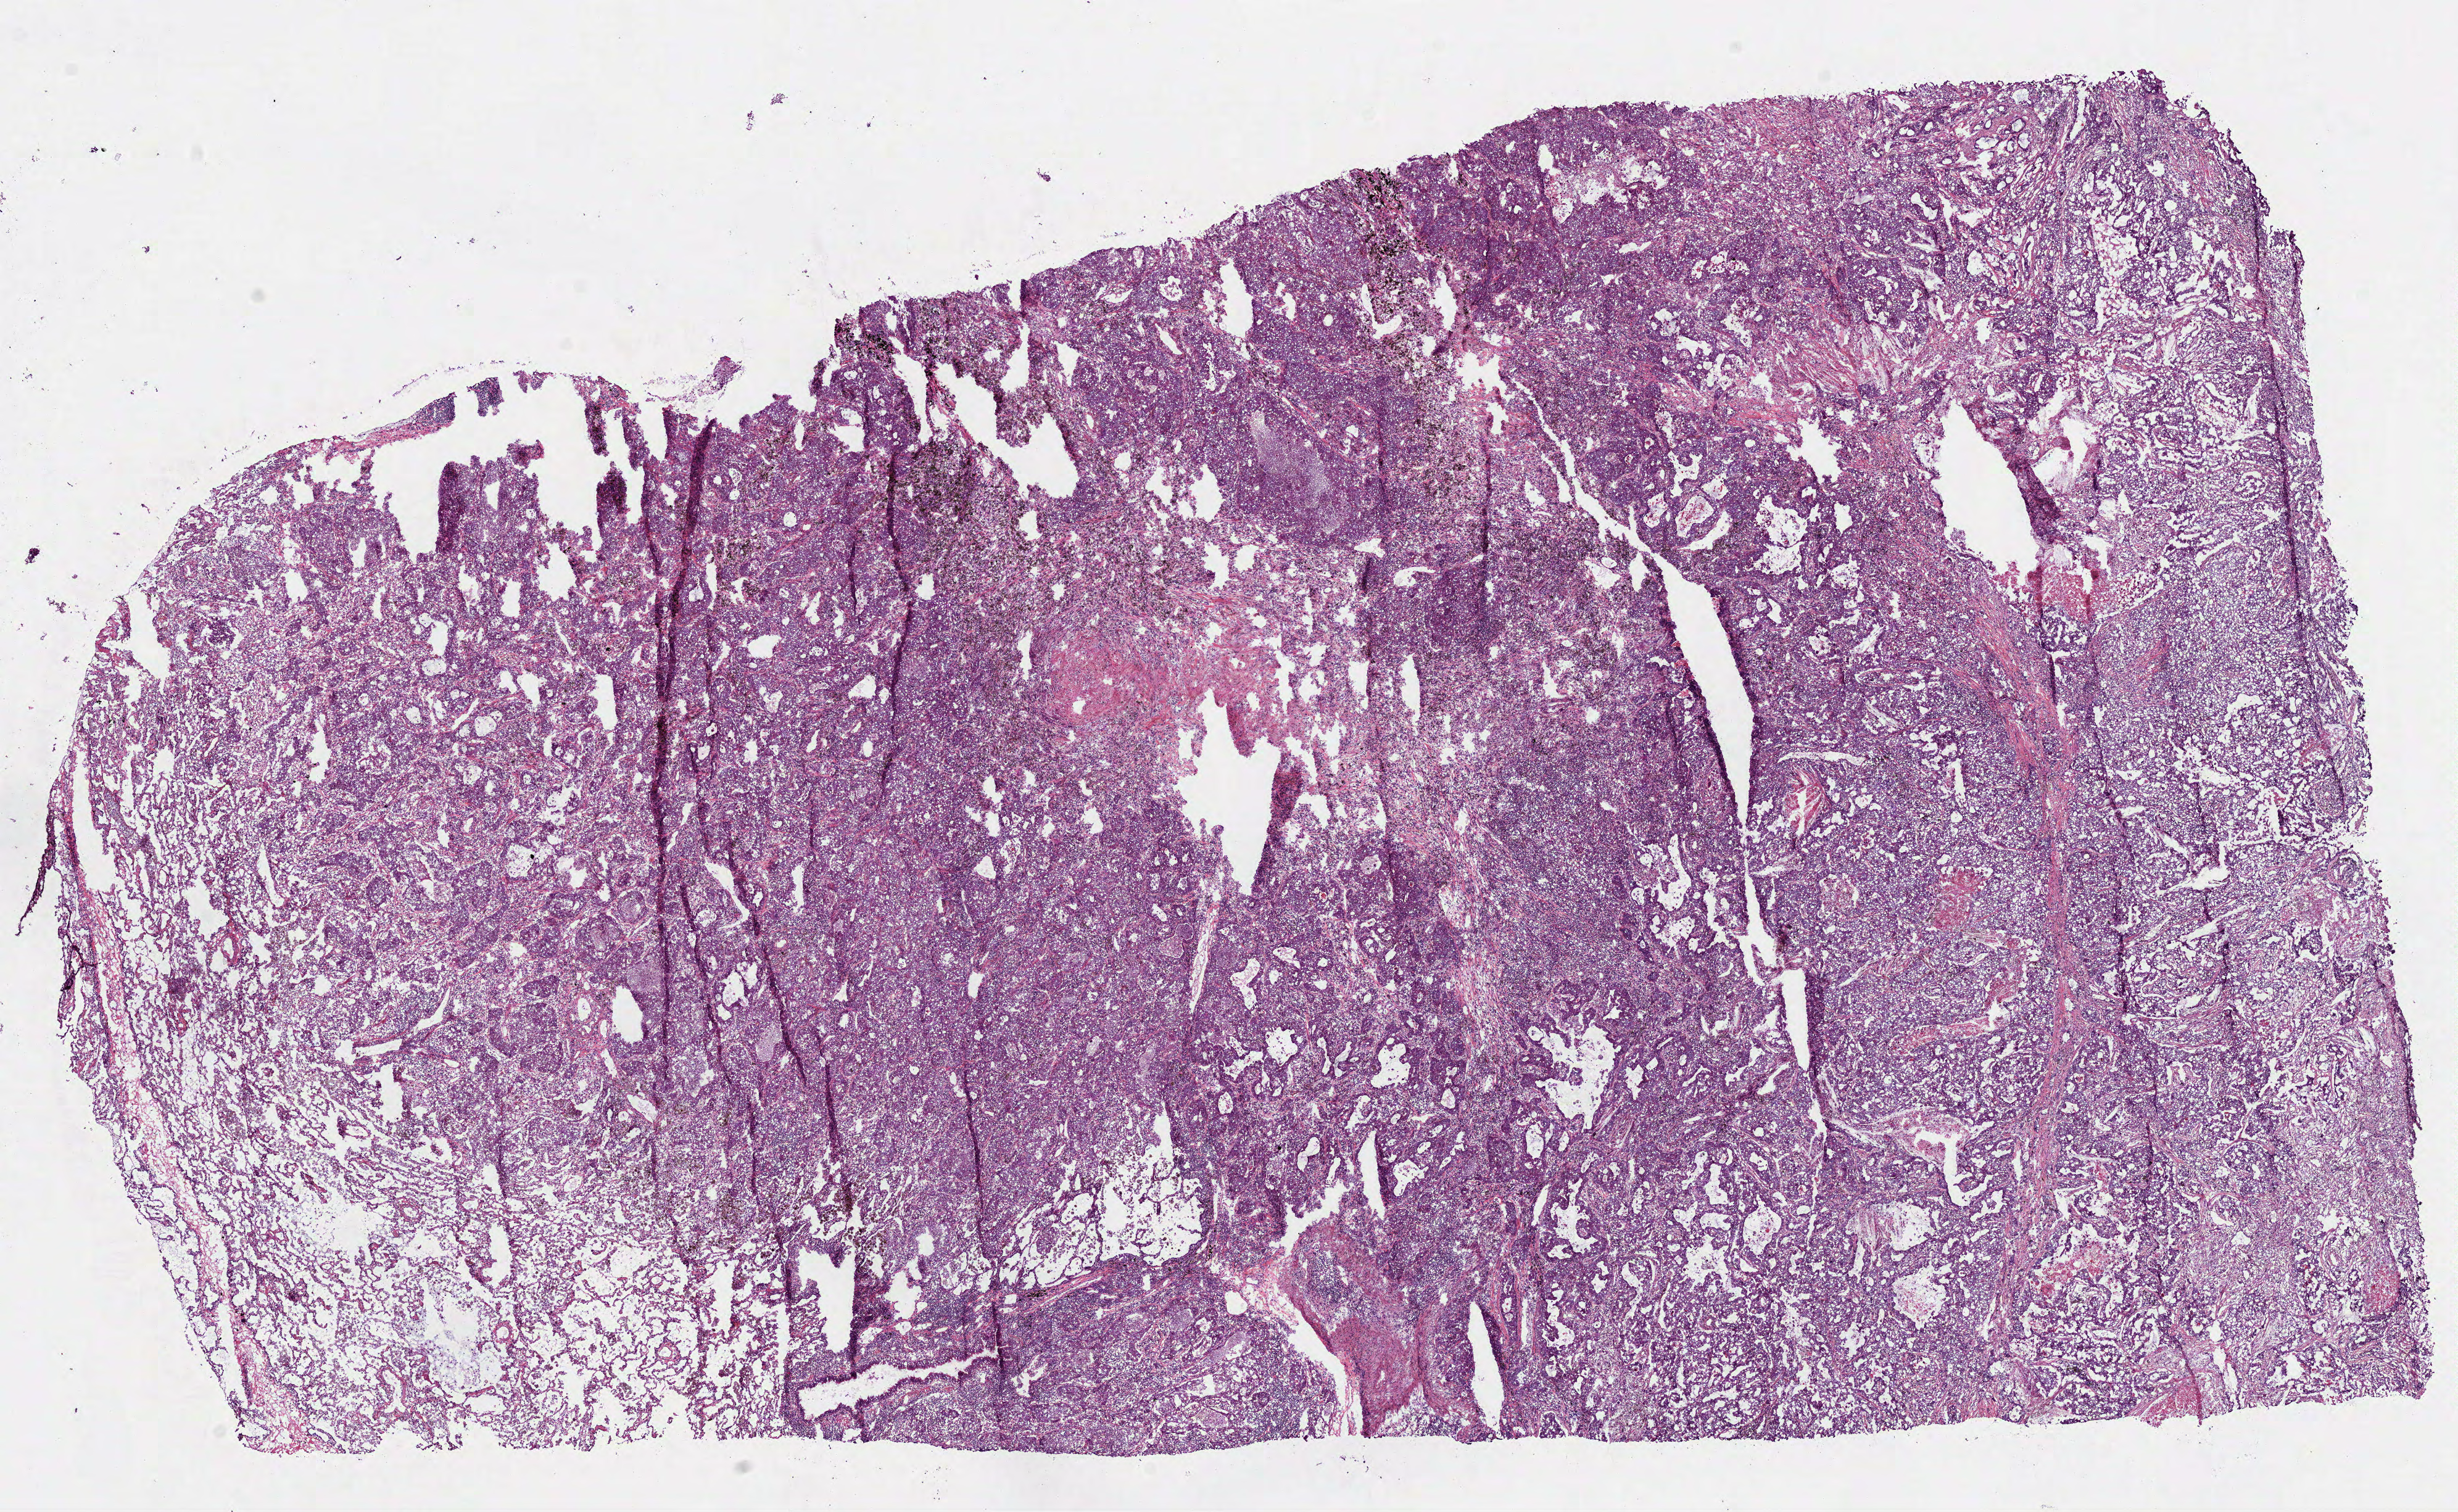
H&E whole-slide image — whole scanned area (about 16.1 x 9.9 mm) shown as a low-resolution overview, frozen section, primary tumour sample from the lung. Male patient; age at initial diagnosis 47 years. Slide review estimates, as recorded: tumour cells 90%, tumour nuclei 65%.
Diagnosis: Adenocarcinoma with mixed subtypes (lower lobe, lung).